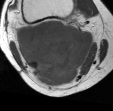
MRI of an extremity soft-tissue mass, one axial slice; slice 26 of 45 in the series (ordered by position); MR volume resampled by the dataset authors to the PET/CT grid (not the native acquisition matrix); 3.27 mm slice thickness; 113 × 111 image matrix, field of view 110 × 108 mm. Female patient. Case-level facts recorded for this patient, not image findings: histological type: liposarcoma; site of the primary tumour: right thigh.
Outlined on this slice (expert contour drawn on MRI and transferred to this co-registered scan by the dataset authors):
- gross tumour volume (mass): bounding box <17,19,95,86> (left, top, right, bottom; pixels)